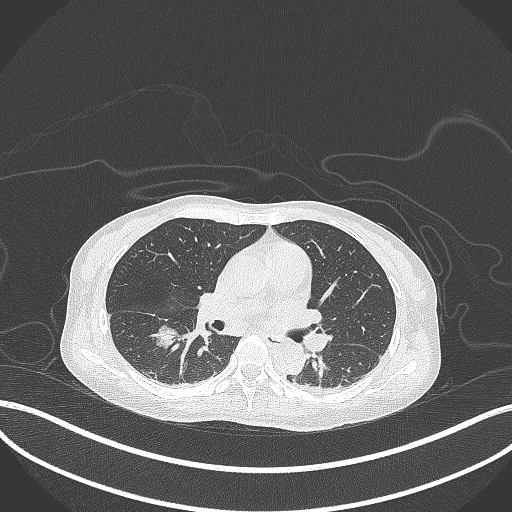
Chest CT, one axial slice. Slice 167 of 261 in the series (ordered by position). Lung window (W 1500 / L -600 HU). 1 mm slice thickness. 512 × 512 image matrix. Female patient, age 44 years. Case-level facts recorded for this patient, not image findings: clinical TNM (as recorded): T1c N0 M0.
Annotated regions visible in this slice (bounding box drawn by a radiologist):
- lung tumour (recorded histology: adenocarcinoma): bounding box (x1, y1, x2, y2) in pixels: (152, 325, 180, 353)